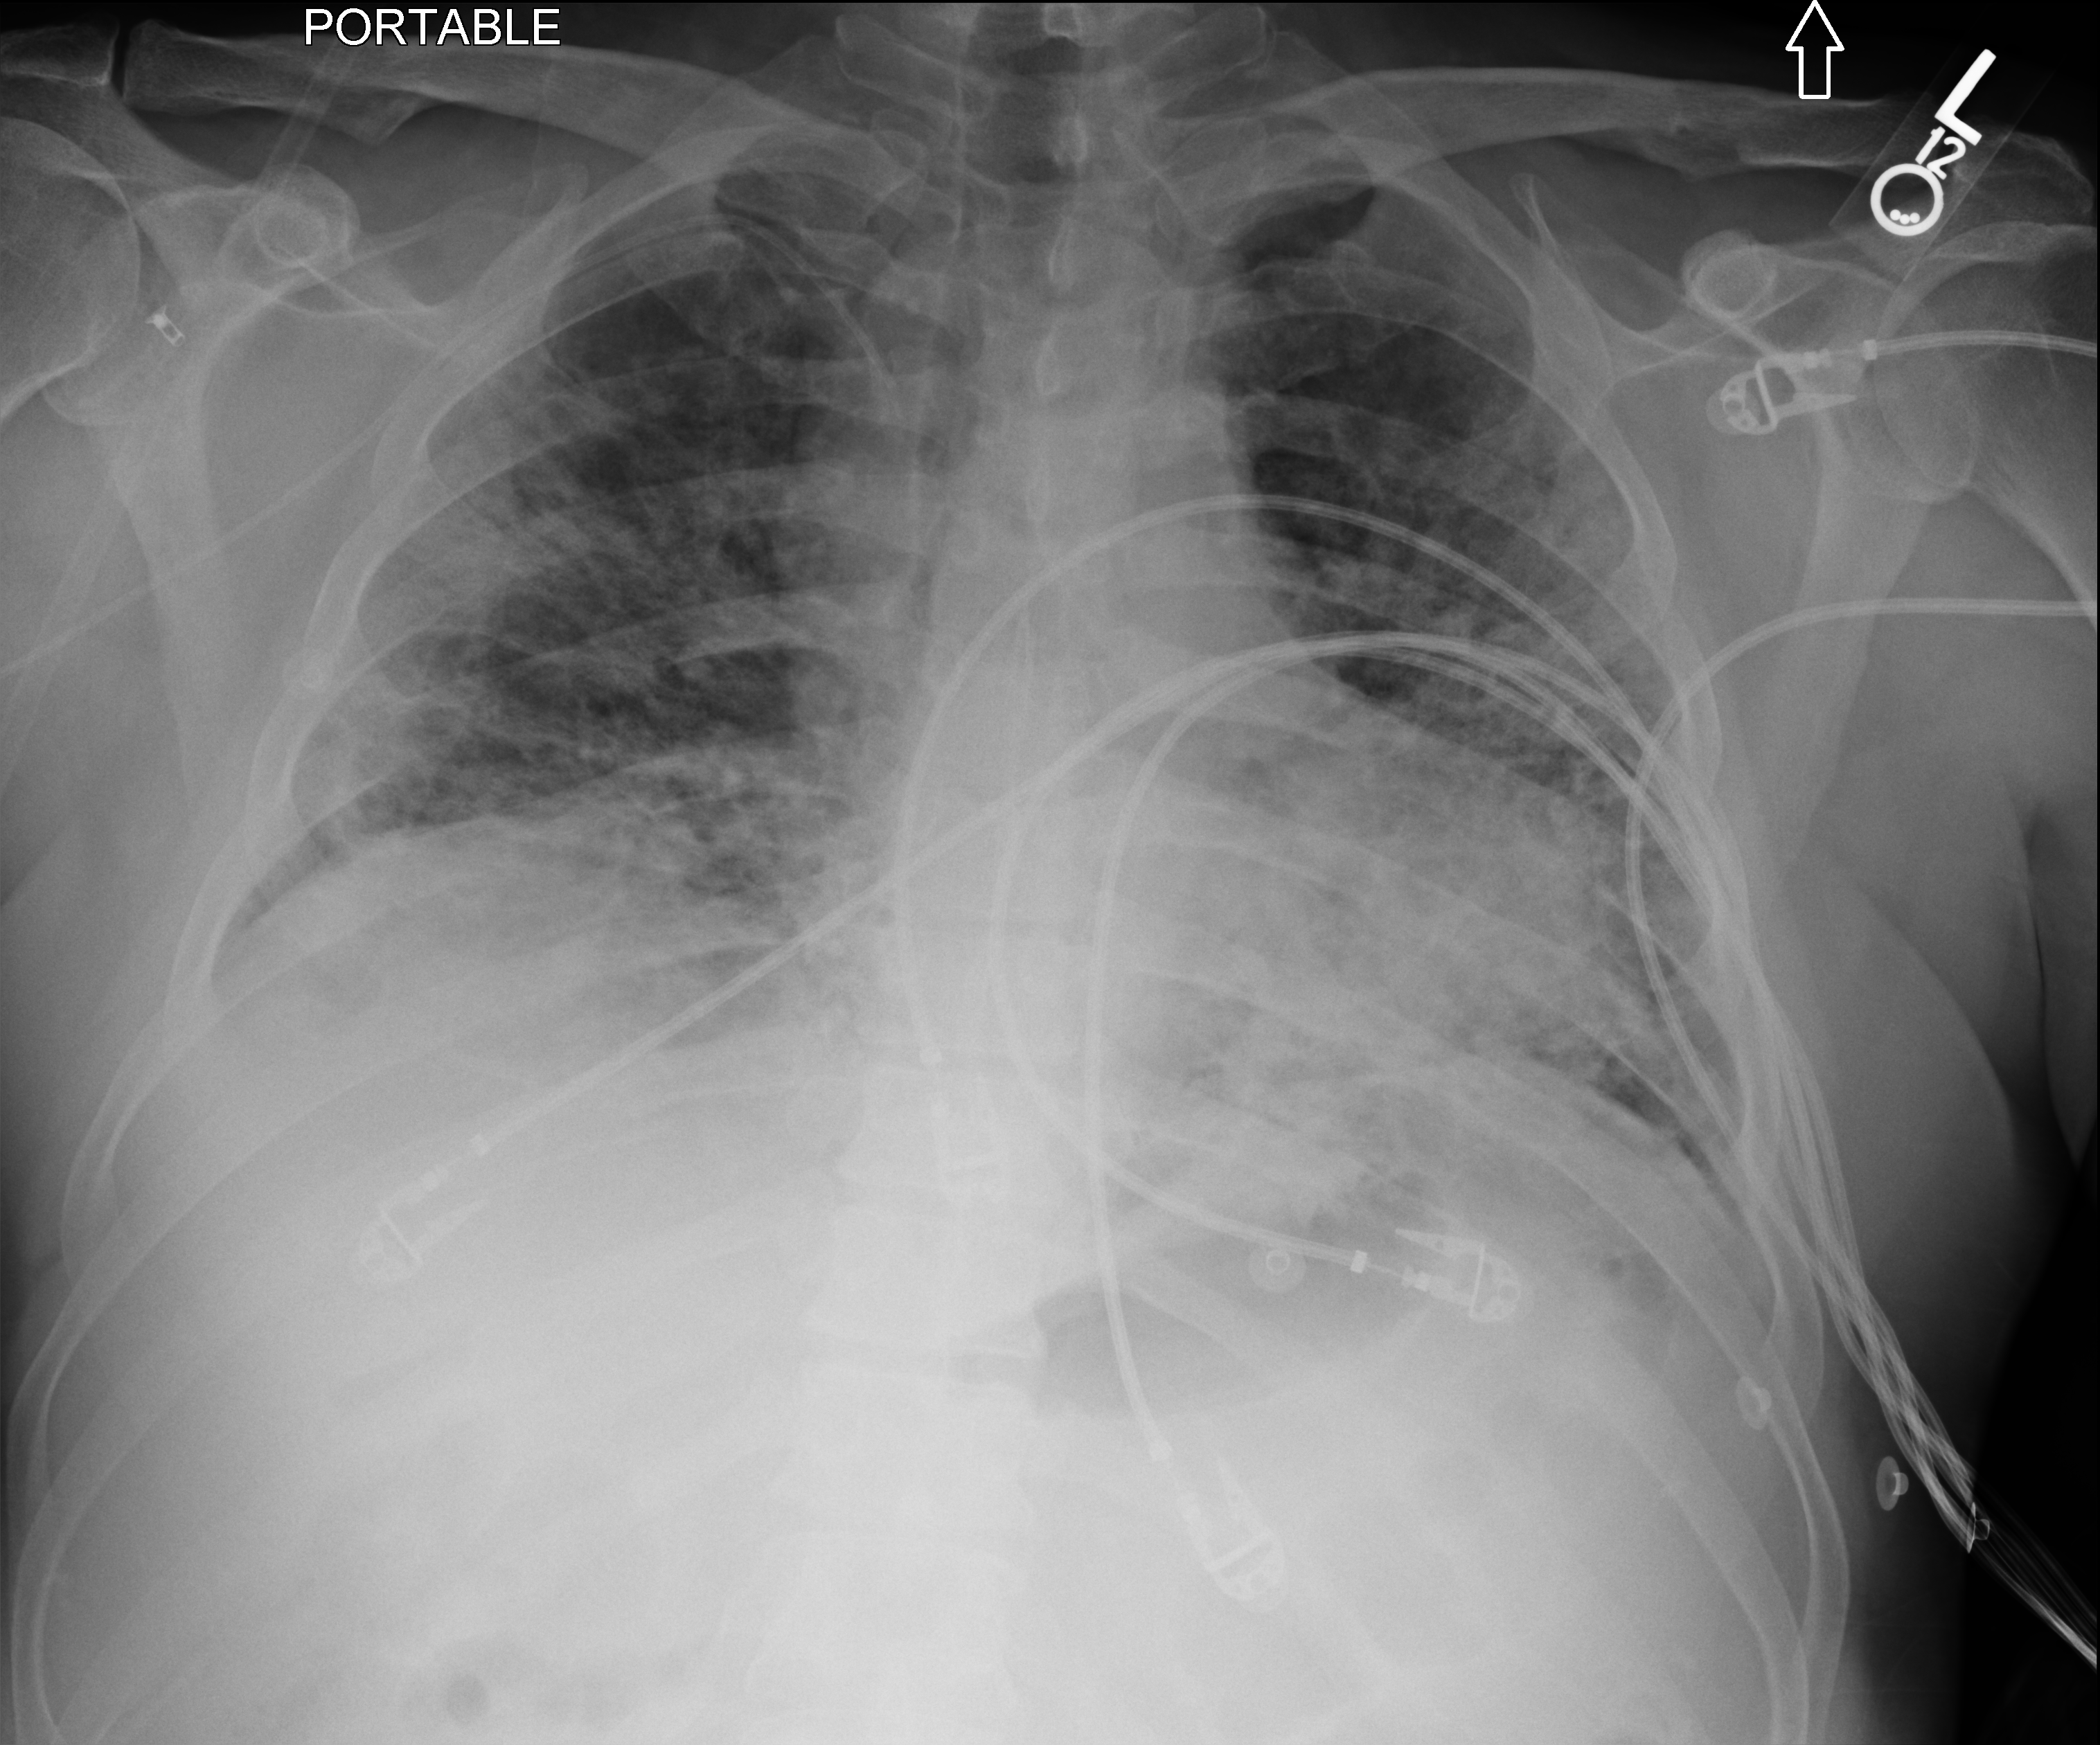
Chest X-ray (portable). Male patient hospitalised with COVID-19, age 18–59 years.
From the hospital-stay record, not from the radiograph (when in the stay this image was taken is not recorded):
- length of hospital stay: 52 days